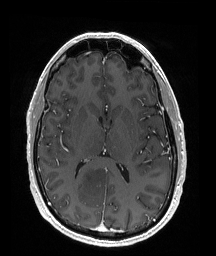
Brain MRI from a brain-tumour surgery series, one axial slice. Slice 89 of 176 in the series (ordered by position). T1-weighted post-contrast. 216 × 256 image matrix, field of view 211 × 250 mm. From the clinical record (not read from this slice): histopathology: Oligodendroglioma; WHO grade: 2; IDH mutation: yes; tumour location: Right Parietal.
Annotated regions visible in this slice (outlined manually by an expert reader):
- tumour: bounding box (x1, y1, x2, y2) in pixels: (70, 164, 111, 203)